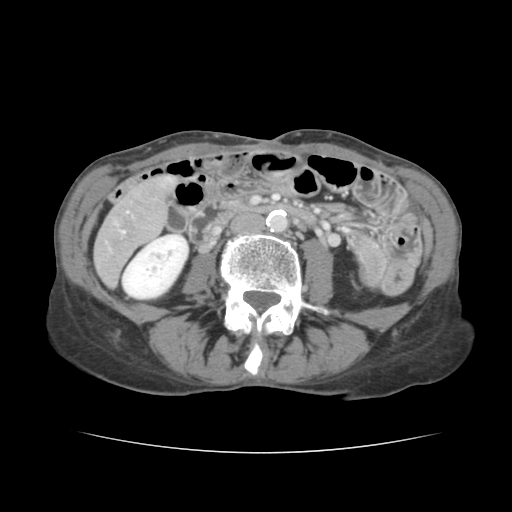
Contrast-enhanced abdominal CT, one axial slice; 120 kVp; soft-tissue window (W 400 / L 40 HU); 2.5 mm slice thickness; 512 × 512 image matrix, field of view 319 × 319 mm. Female patient, age 77 years. Case-level facts recorded for this patient, not image findings: diagnosis: colorectal cancer liver metastases, imaged before liver resection; multiple liver metastases: yes; largest metastasis: 3 cm; disease in both lobes: no.
Annotated regions visible in this slice (outlined manually by an expert reader):
- liver: bounding box (x1, y1, x2, y2) in pixels: (95, 178, 173, 284)
- portal vein (with intrahepatic branches): (122, 231, 124, 233)